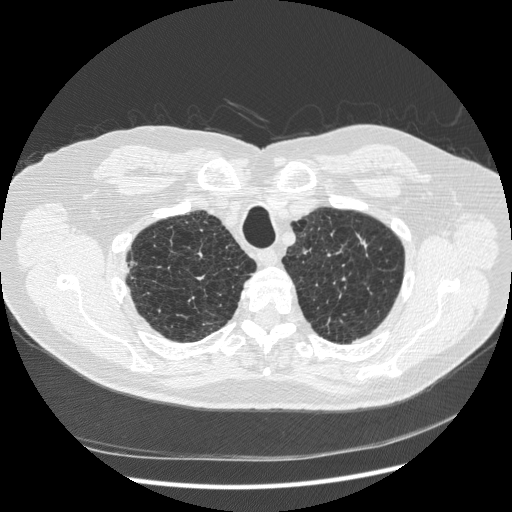
Low-dose screening chest CT, axial slice, first (baseline) screen, lung window (W 1500 / L -600 HU), standard (soft-tissue) reconstruction kernel (STANDARD), slice 42 of 265 in the series, 512 × 512 image matrix, field of view 380 × 380 mm. Male participant, aged 70 years at enrolment. Former smoker at enrolment.
Lesion marked by an expert reader, bounding box [x1, y1, x2, y2] px = [332, 217, 387, 272]. The screening reader recorded 2 non-calcified nodules or masses ≥4 mm on this exam (right lower lobe, right lower lobe); which of them this box marks is not recorded. Later outcome: lung cancer diagnosed 816 days after this screen (after the third annual screen) — squamous cell carcinoma, NOS, left upper lobe, moderately differentiated (G2), stage IA (AJCC 6th edition), 18 mm at pathology.